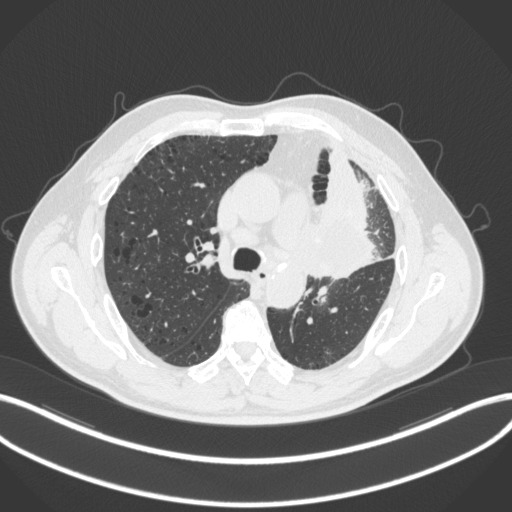
Chest CT, one axial slice. Position 190 of 286 along the scan axis. Reconstruction kernel B31f. Lung window (W 1500 / L -600 HU). 512 × 512 image matrix, field of view 400 × 400 mm. Male patient, age 68 years. From the clinical record (not read from this slice): clinical TNM (as recorded): T3 N3 M1.
Annotated regions visible in this slice (bounding box drawn by a radiologist):
- lung tumour (recorded histology: adenocarcinoma): bounding box (x1, y1, x2, y2) in pixels: (298, 193, 376, 279)